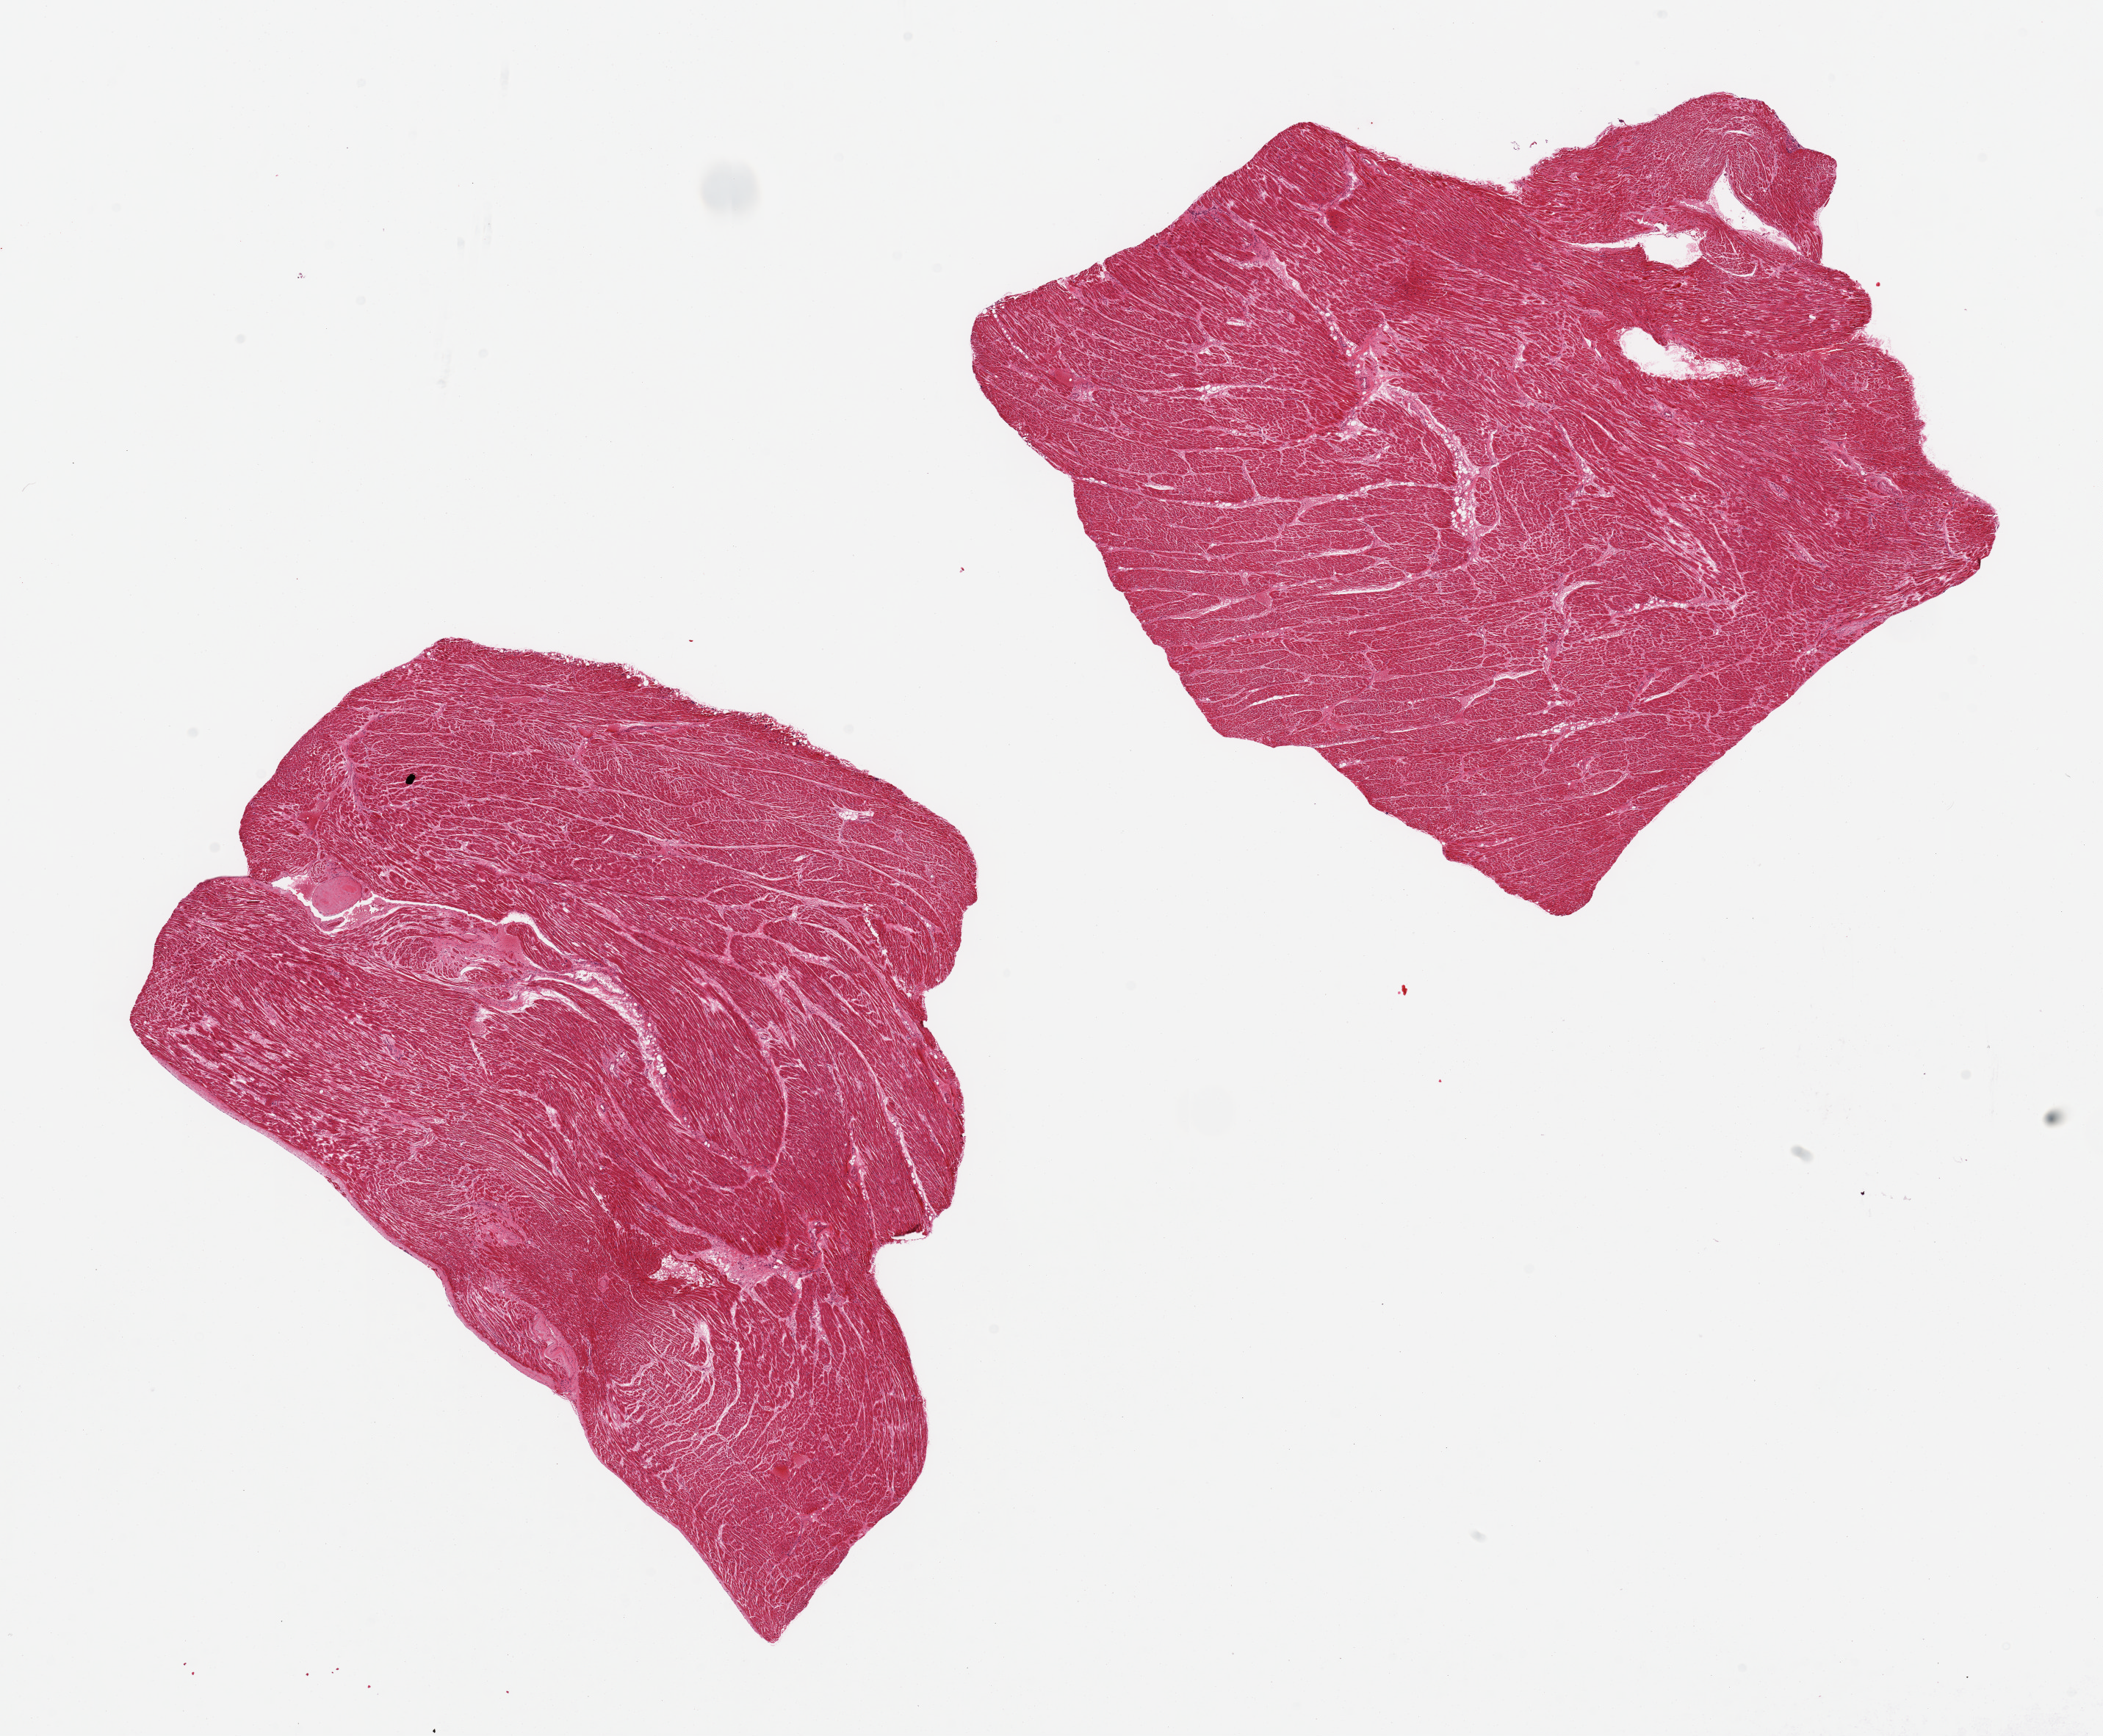
Whole-slide image, hematoxylin and eosin (H&E) stain — a low-resolution overview of the entire scanned area, about 22.6 x 18.7 mm (from a 20x scan), PAXgene-fixed, paraffin-embedded tissue, section of heart (target tissue), donor tissue sample. Donor: female.
- review note (as recorded): 2 pieces, minimal fibrosis, focal microinfarct